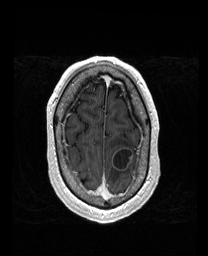
Brain MRI from a brain-tumour surgery series, one axial slice; slice 148 of 192 in the series (ordered by position); T1-weighted post-contrast; 1 mm slice thickness; 208 × 256 image matrix. From the clinical record (not read from this slice): histopathology: Metastatic Carcinoma from Lung Adenocarcinoma; tumour location: Left Frontal.
Annotated regions visible in this slice (expert manual segmentation):
- tumour: bounding box <113,147,133,171> (left, top, right, bottom; pixels)